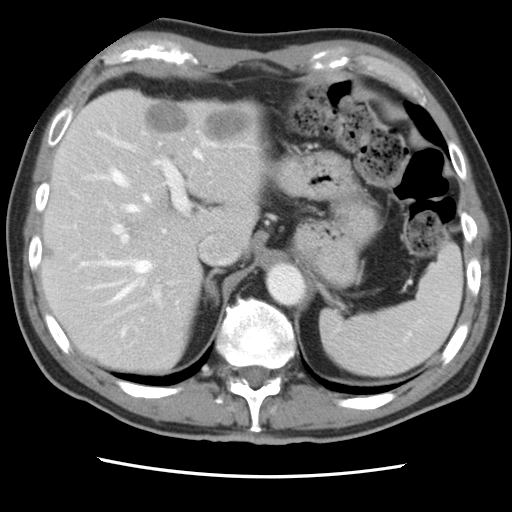
Contrast-enhanced abdominal CT, one axial slice. Position 60 of 83 along the scan axis. 120 kVp. Intravenous contrast given. Soft-tissue window (W 400 / L 40 HU). 5 mm slice thickness. 512 × 512 image matrix, field of view 321 × 321 mm. Male patient, age 69 years. Case-level facts recorded for this patient, not image findings: diagnosis: colorectal cancer liver metastases, imaged before liver resection; multiple liver metastases: yes; largest metastasis: 3.5 cm.
Outlined on this slice (outlined manually by an expert reader):
- hepatic veins: bounding box (x1, y1, x2, y2) in pixels: (82, 150, 201, 335)
- liver: (43, 90, 262, 372)
- planned liver remnant (the part of the liver to remain after resection): (43, 143, 209, 372)
- portal vein (with intrahepatic branches): (107, 130, 248, 304)
- liver metastasis: (146, 104, 190, 133)
- liver metastasis: (205, 108, 250, 140)